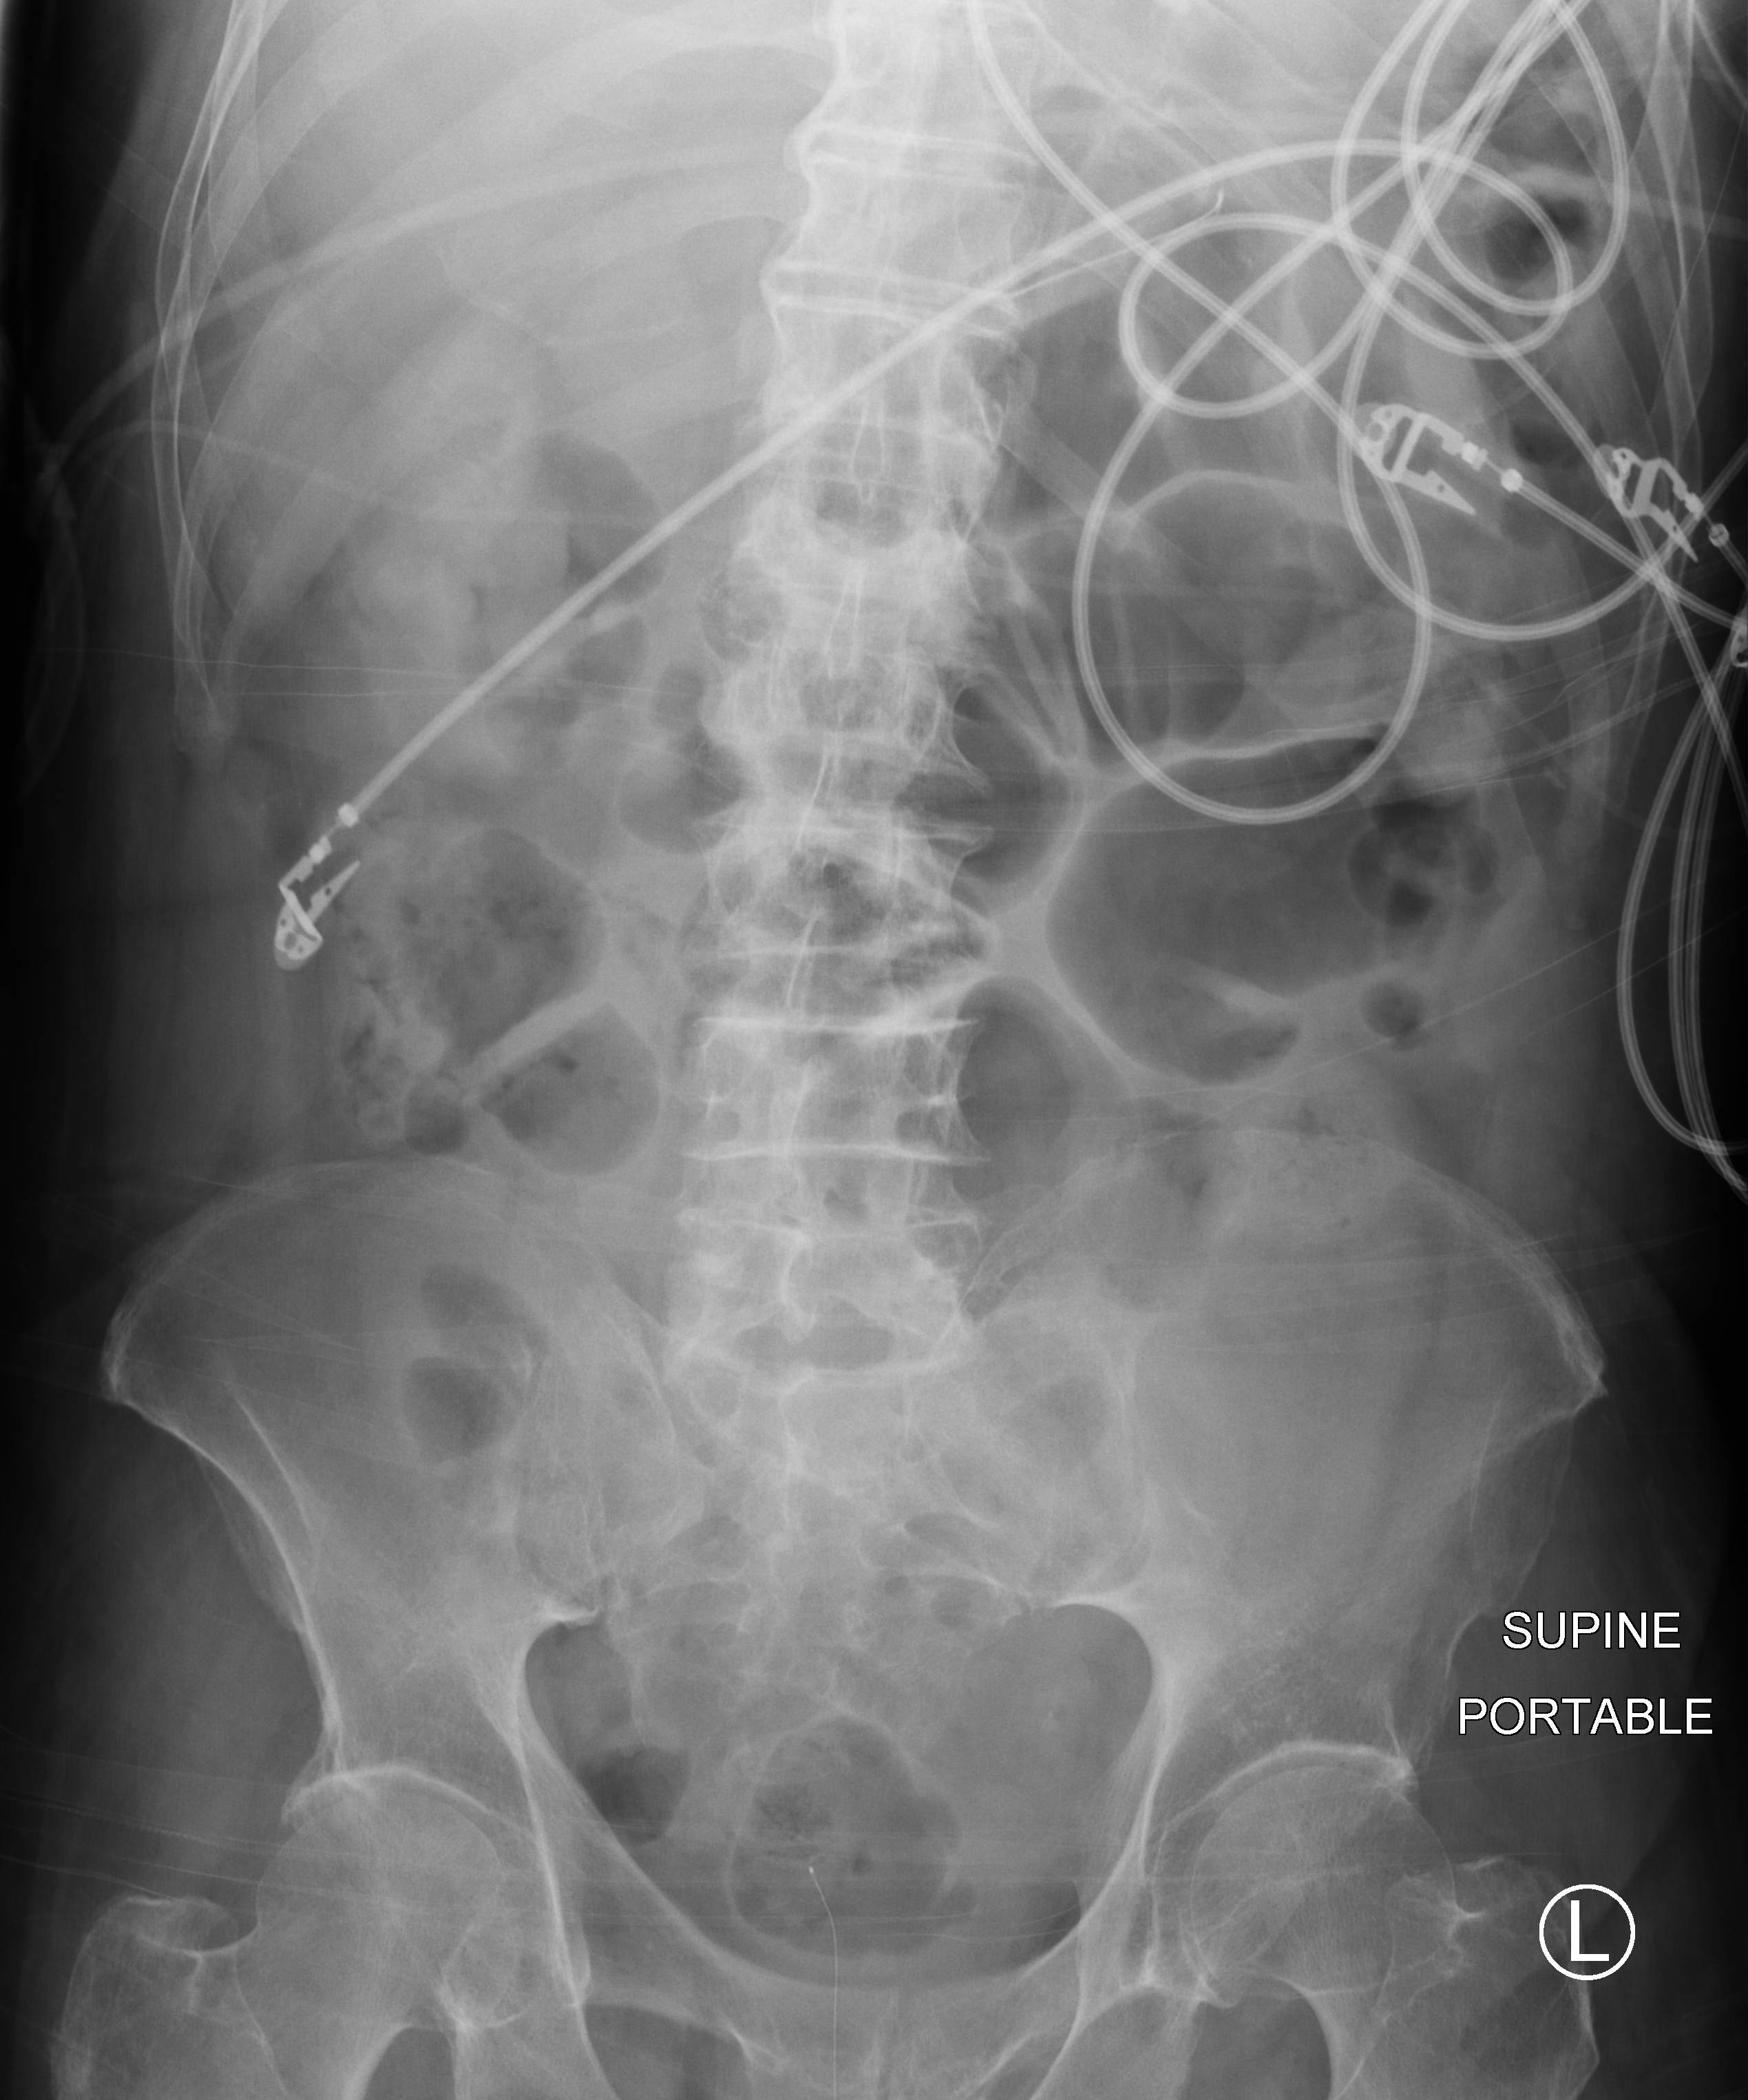
Bedside abdomen radiograph (computed radiography), anteroposterior (AP) projection. Patient hospitalised with COVID-19; male, aged 75–90 years.
Hospital-stay facts (about this admission, not read from this image; timing relative to this image not recorded):
- mechanically ventilated during this hospital stay: yes
- diabetes (admission record): no